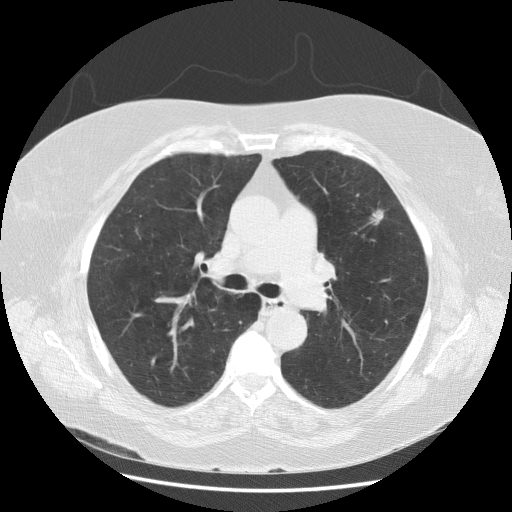
Low-dose screening chest CT, one axial slice. Position 102 of 164 along the scan axis. 120 kVp. Lung window (W 1500 / L -600 HU). 512 × 512 image matrix, field of view 380 × 380 mm.
Outlined on this slice (expert manual segmentation):
- lesion 1 (tumor, upper lobe of left lung): box from (x=370, y=210) to (x=384, y=225) px